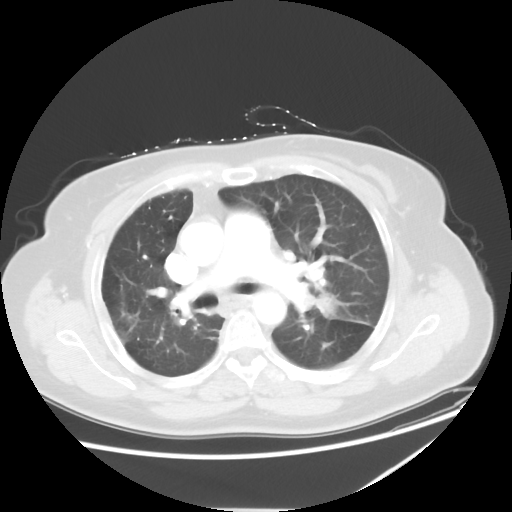
Chest CT, one axial slice. Slice 35 of 54 in the series (ordered by position). 120 kVp. Lung window (W 1500 / L -600 HU). 5 mm slice thickness. 512 × 512 image matrix, field of view 384 × 384 mm. Patient: female, 61 years. From the clinical record (not read from this slice): clinical TNM (as recorded): T1c N3 M1.
Structures marked on this image (rectangle marked by the reading radiologist):
- lung tumour (recorded histology: adenocarcinoma): bounding box [x1, y1, x2, y2] px = [315, 289, 377, 331]